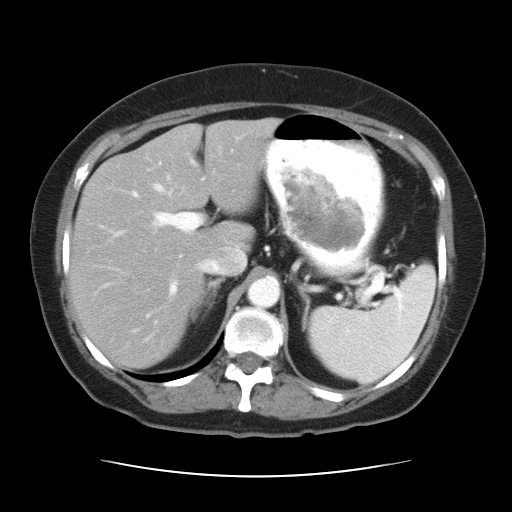
Contrast-enhanced abdominal CT, one axial slice. Position 21 of 34 along the scan axis. Reconstruction kernel STANDARD. 120 kVp. Soft-tissue window (W 400 / L 40 HU). 7.5 mm slice thickness. 512 × 512 image matrix, field of view 360 × 360 mm. Female patient, age 65 years. From the clinical record (not read from this slice): diagnosis: colorectal cancer liver metastases, imaged before liver resection; multiple liver metastases: yes; largest metastasis: 2.2 cm.
Structures marked on this image (outlined manually by an expert reader):
- hepatic veins: bounding box [x1, y1, x2, y2] px = [152, 175, 246, 274]
- liver: [70, 121, 273, 368]
- planned liver remnant (the part of the liver to remain after resection): [70, 121, 273, 361]
- portal vein (with intrahepatic branches): [108, 150, 233, 318]